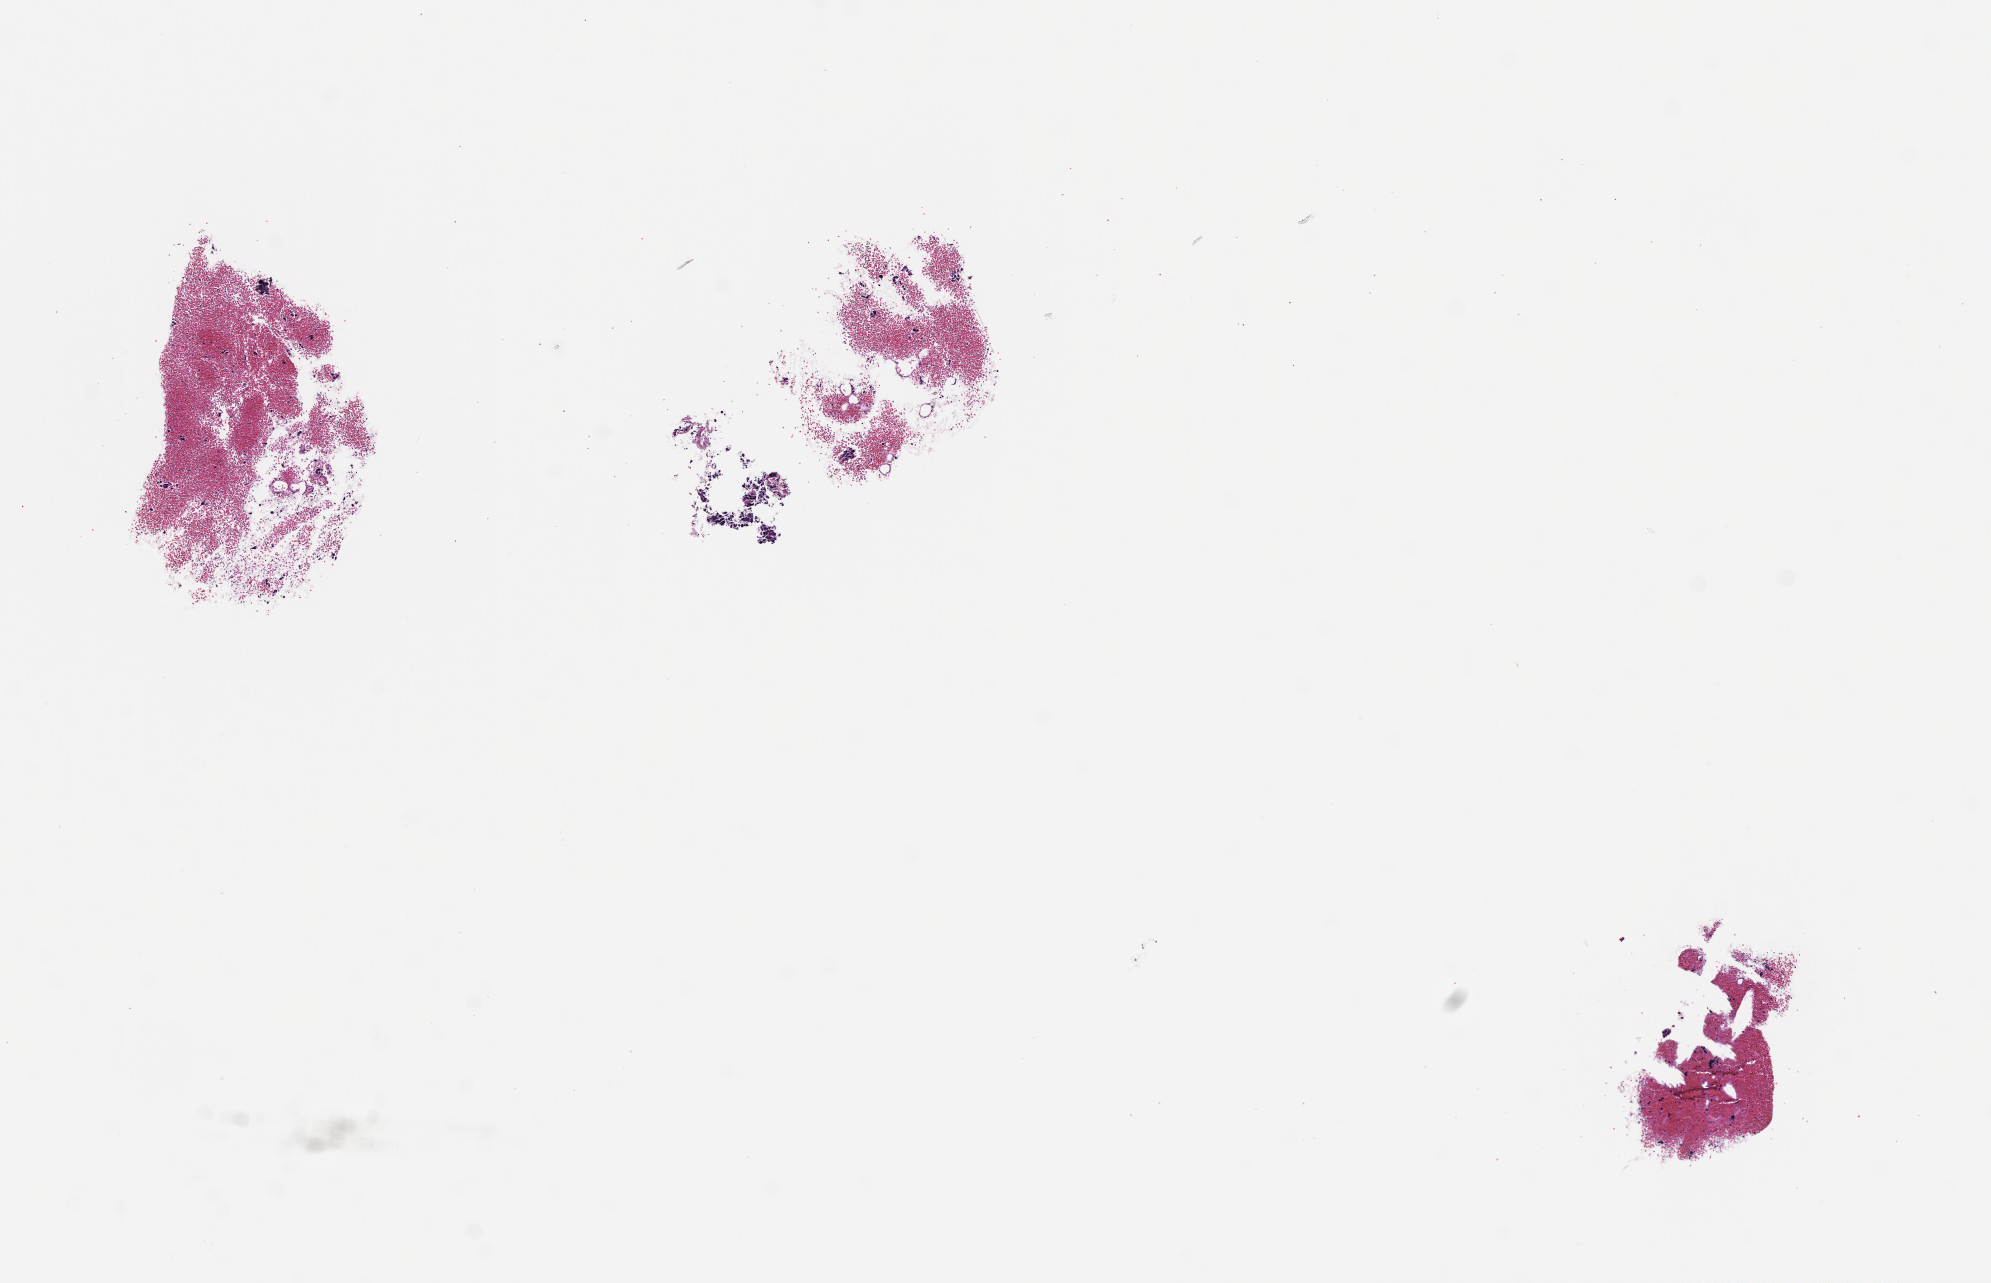
Whole-slide image, H&E stain, low-resolution overview of the scanned area, about 8.0 x 5.2 mm; FFPE section; tissue site: lung; specimen time point: collected at baseline (before treatment). Female patient.
* this section: primary tumour tissue
* diagnosis: Non-Small Cell Lung Carcinoma